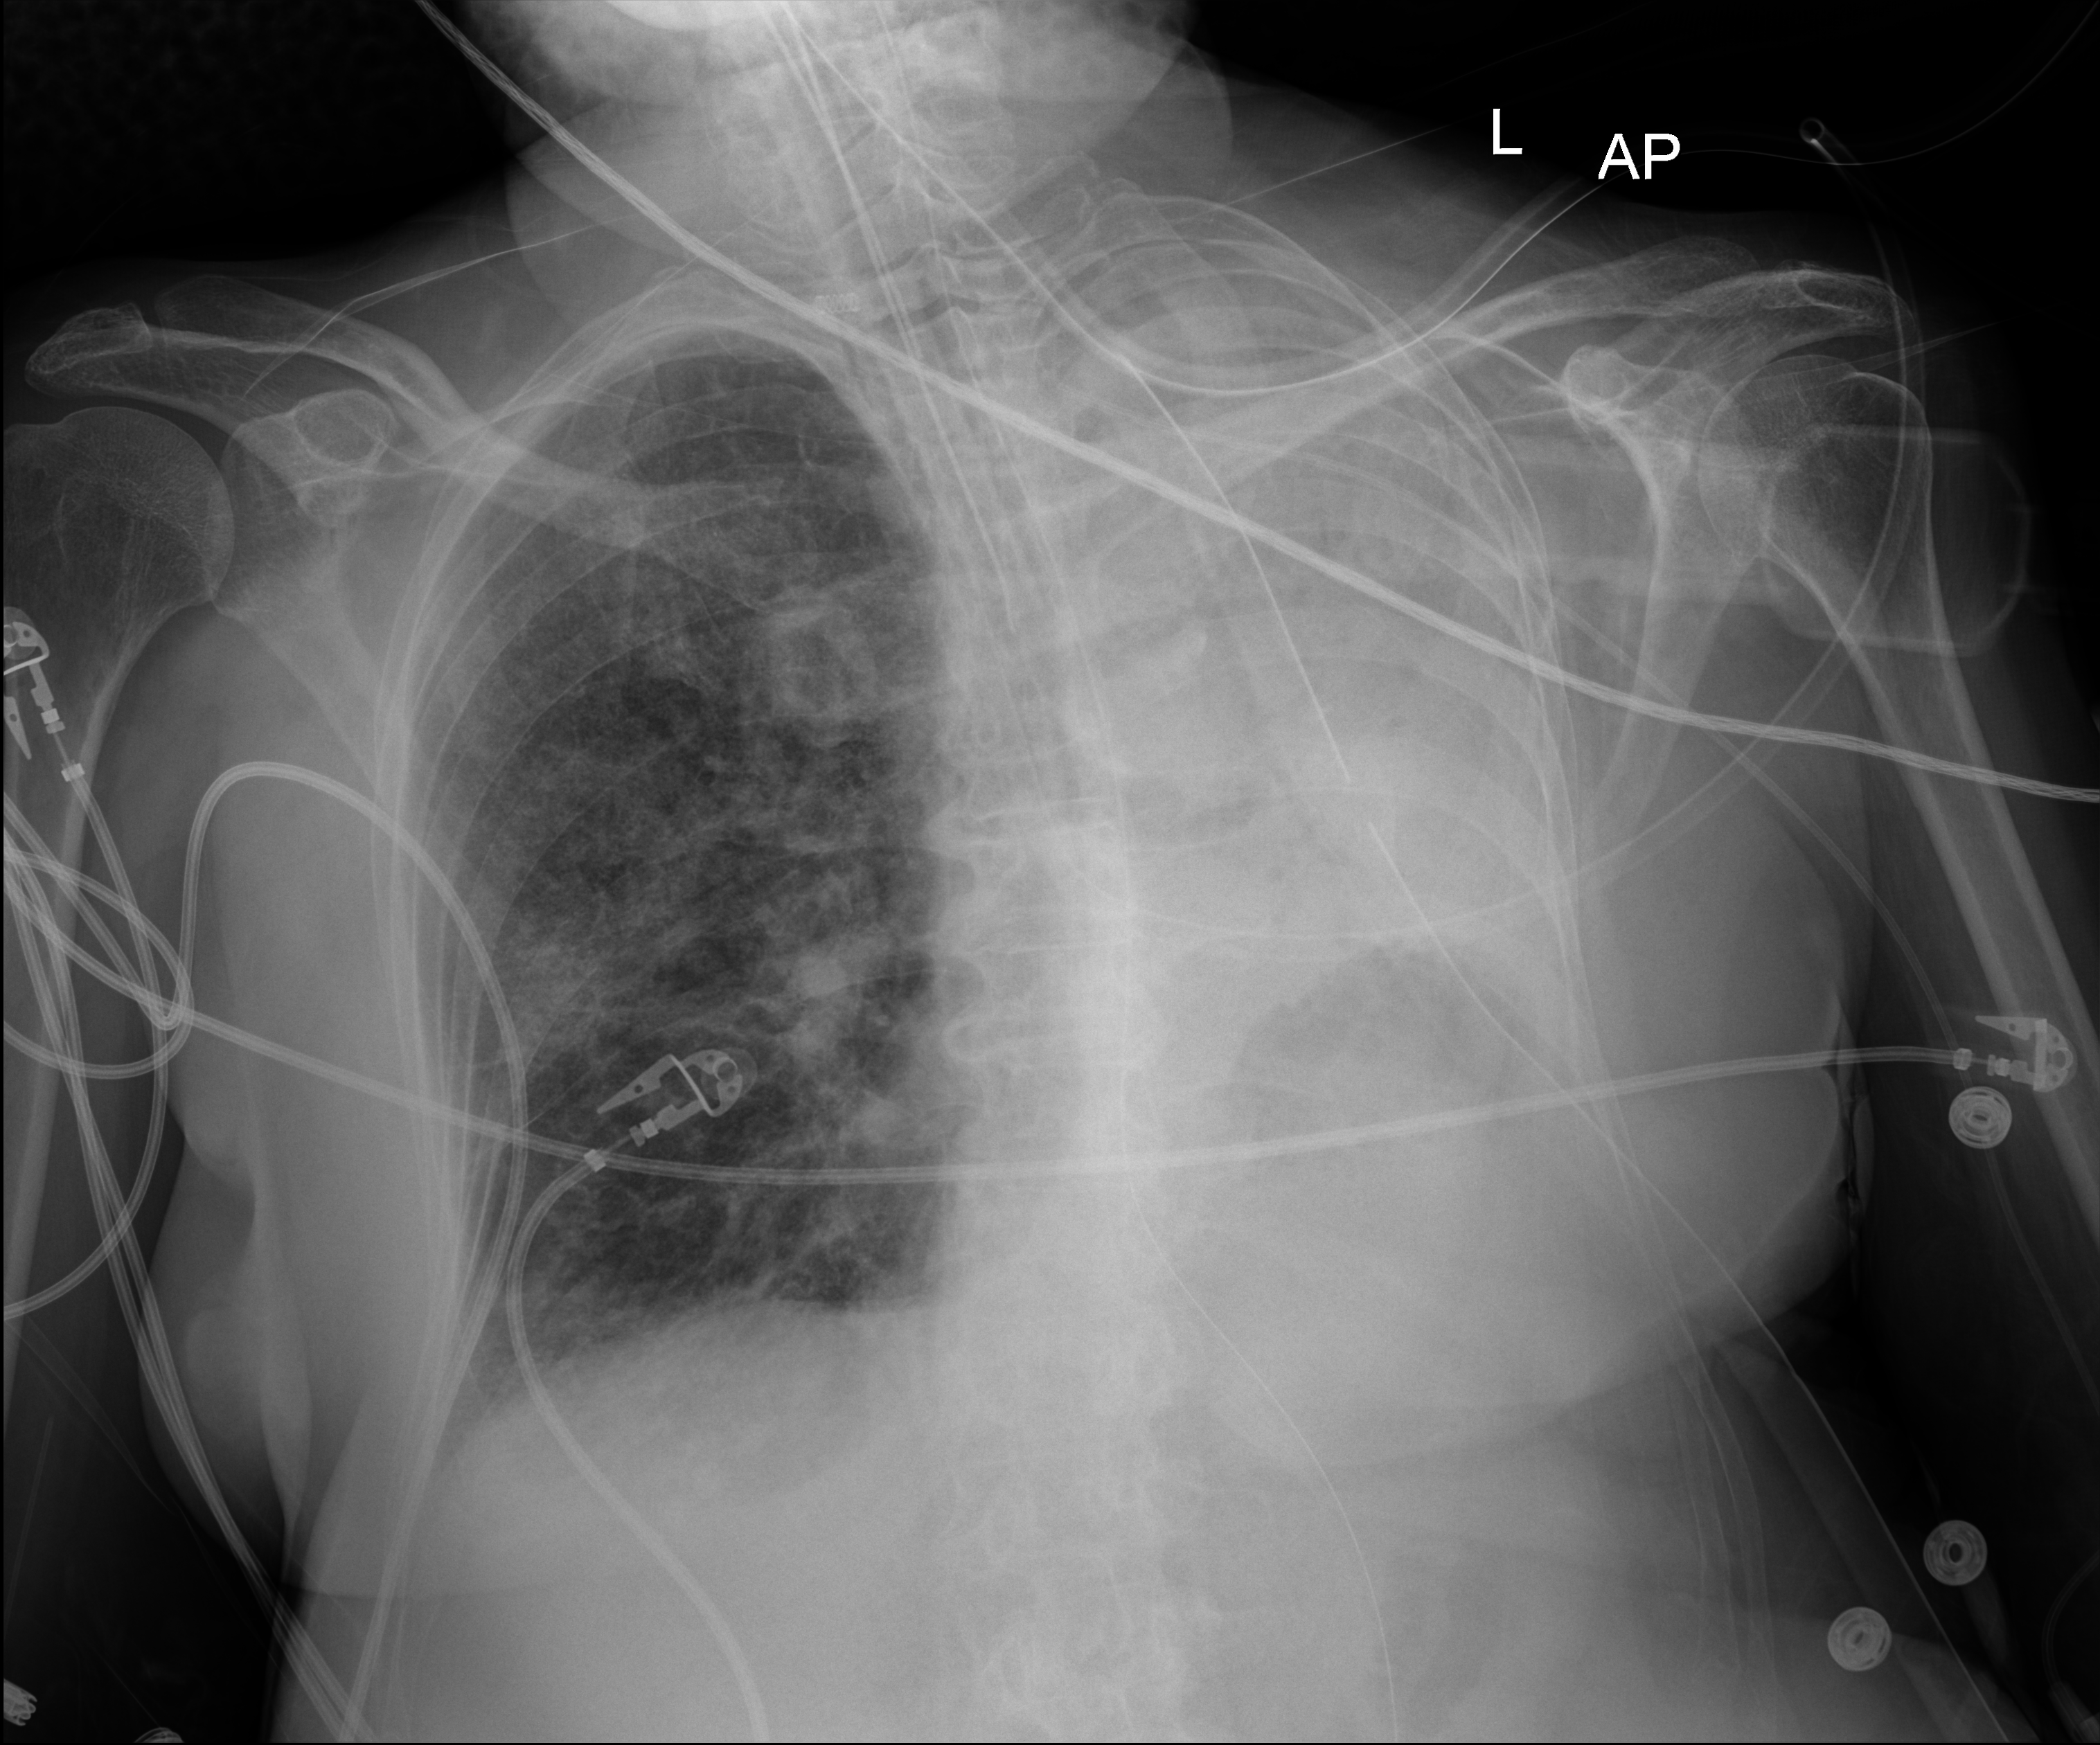
Bedside chest radiograph (digital radiography), anteroposterior (AP) projection. Female patient hospitalised with COVID-19, age 75–90 years.
Hospital-stay facts (about this admission, not read from this image; timing relative to this image not recorded): other chronic lung disease (admission record): yes; length of hospital stay: 70 days.